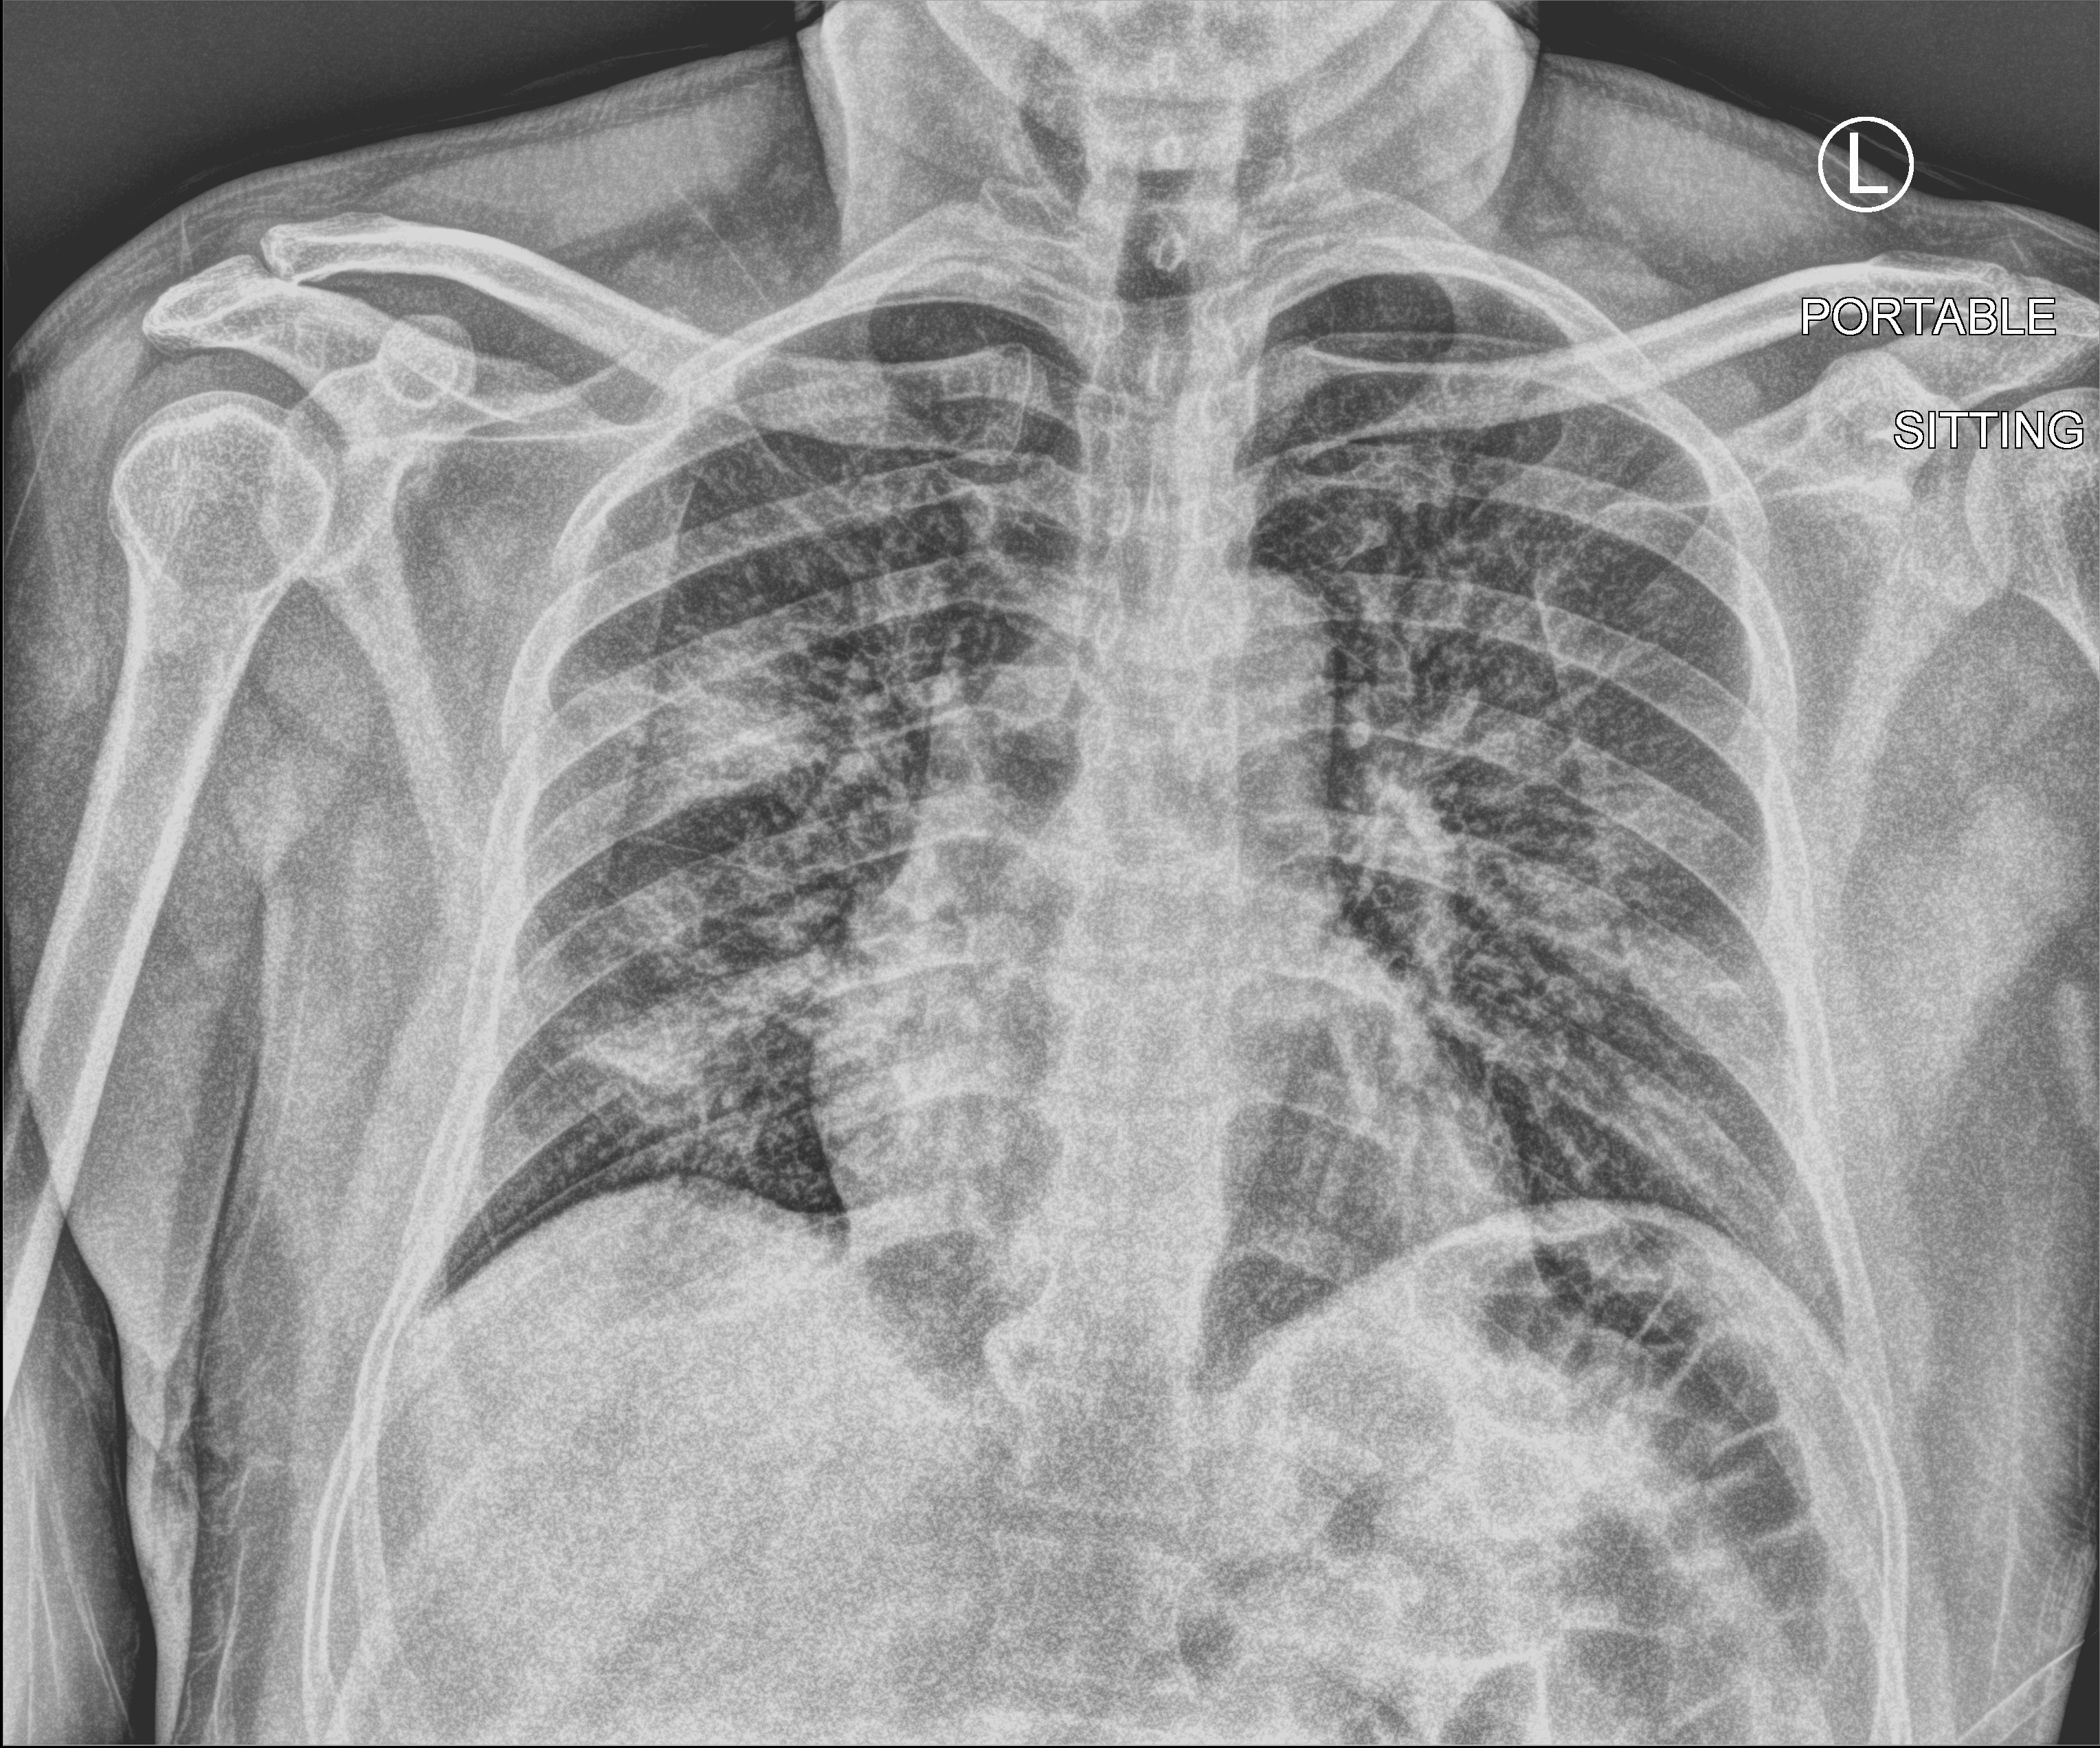
Bedside chest radiograph (computed radiography), anteroposterior (AP) projection. Patient hospitalised with COVID-19; male, aged 18–59 years.
Hospital-stay facts (about this admission, not read from this image; timing relative to this image not recorded): mechanically ventilated during this hospital stay: no; length of hospital stay: 1 day.